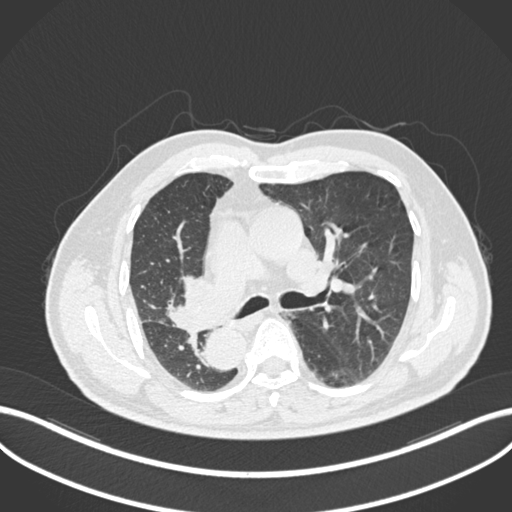
Chest CT, one axial slice. Position 138 of 206 along the scan axis. Reconstruction kernel B30f. Lung window (W 1500 / L -600 HU). 512 × 512 image matrix, field of view 400 × 400 mm. Patient: male, 67 years. From the clinical record (not read from this slice): clinical TNM (as recorded): T2a N0 M0.
Structures marked on this image (rectangle marked by the reading radiologist):
- lung tumour (recorded histology: squamous cell carcinoma): bounding box <161,272,231,335> (left, top, right, bottom; pixels)